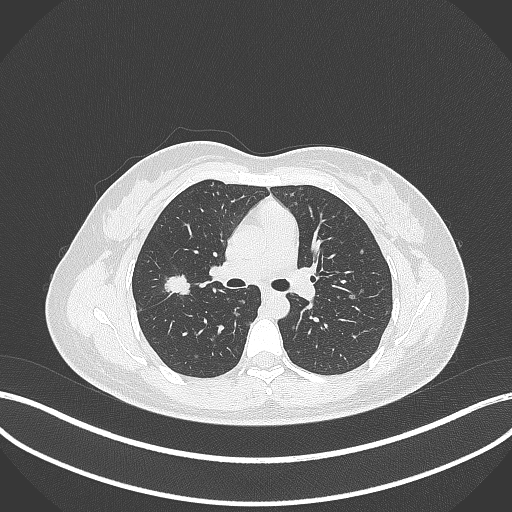
Chest CT, one axial slice. Slice 203 of 307 in the series (ordered by position). Lung window (W 1500 / L -600 HU). 512 × 512 image matrix. Female patient, age 33 years. From the clinical record (not read from this slice): clinical TNM (as recorded): T1c N0 M0.
Outlined on this slice (bounding box drawn by a radiologist):
- lung tumour (recorded histology: adenocarcinoma): bounding box [x1, y1, x2, y2] px = [162, 275, 190, 296]